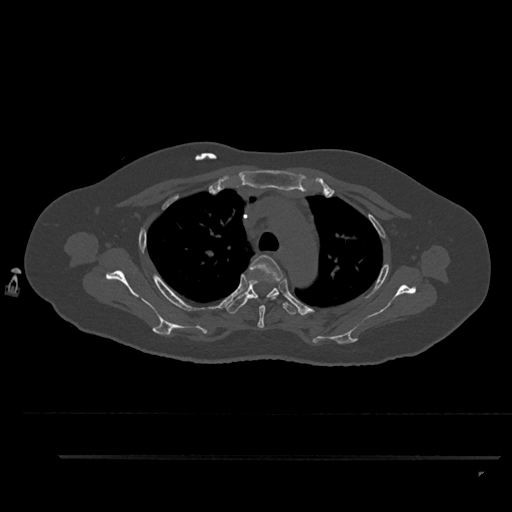
CT including the spine, one axial slice; position 662 of 797 along the scan axis; reconstruction kernel Br40s/3; 120 kVp; bone window (W 1800 / L 400 HU); 0.5 mm slice thickness; 512 × 512 image matrix, field of view 408 × 408 mm. Patient: female, 44 years. From the clinical record (not read from this slice): primary cancer: renal.
Annotated regions visible in this slice (semi-automatic segmentation, software-assisted and operator-edited):
- T3 vertebra: bounding box (x1, y1, x2, y2) in pixels: (249, 255, 283, 328)
- T4 vertebra: (226, 279, 300, 315)